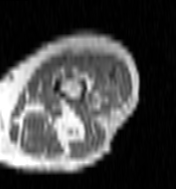
MRI of an extremity soft-tissue mass, one axial slice; position 29 of 100 along the scan axis; MR volume resampled by the dataset authors to the PET/CT grid (not the native acquisition matrix); 3.27 mm slice thickness; 176 × 189 image matrix, field of view 172 × 185 mm. Female patient. From the clinical record (not read from this slice): histological type: undifferentiated – high grade; grade: high; site of the primary tumour: left thigh.
Outlined on this slice (expert contour drawn on MRI and transferred to this co-registered scan by the dataset authors):
- gross tumour volume including surrounding oedema: bounding box <66,55,122,104> (left, top, right, bottom; pixels)